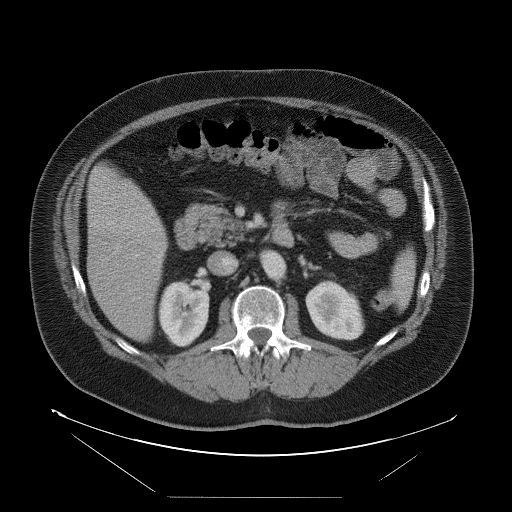
Contrast-enhanced abdominal CT, one axial slice. Slice 38 of 114 in the series (ordered by position). 120 kVp. Intravenous contrast given. Soft-tissue window (W 400 / L 40 HU). 512 × 512 image matrix, field of view 500 × 500 mm. Male patient, age 61 years. Case-level facts recorded for this patient, not image findings: diagnosis: colorectal cancer liver metastases, imaged before liver resection; multiple liver metastases: no; largest metastasis: 6.5 cm; chemotherapy before resection: no.
Outlined on this slice (manually delineated by an expert):
- liver: bounding box <88,166,167,341> (left, top, right, bottom; pixels)